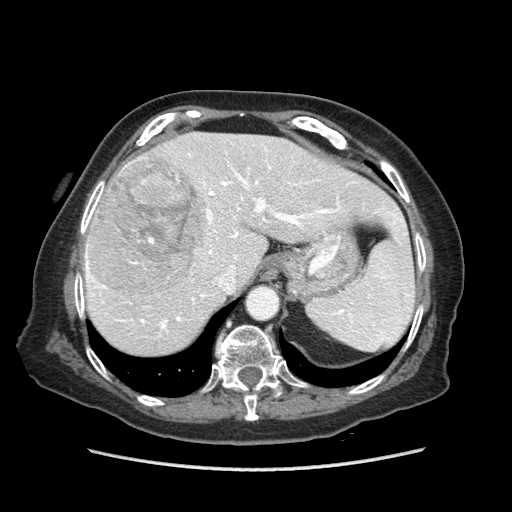
Contrast-enhanced abdominal CT (liver protocol), one axial slice. Position 61 of 89 along the scan axis. Reconstruction kernel STANDARD. Soft-tissue window (W 400 / L 40 HU). 2.5 mm slice thickness. 512 × 512 image matrix, field of view 360 × 360 mm. From the clinical record (not read from this slice): diagnosis: hepatocellular carcinoma (patient treated with transarterial chemoembolisation; whether this scan precedes or follows treatment is not stated here); TNM stage (as recorded): Stage-IIIA; Child-Pugh class: A.
Outlined on this slice (semi-automatically segmented with operator editing):
- liver parenchyma outside the tumour (the mass and vessels are separate outlines, so this box may not span the whole liver): bounding box [x1, y1, x2, y2] px = [84, 132, 402, 354]
- mass: [87, 159, 209, 294]
- liver vessels: [85, 149, 399, 330]